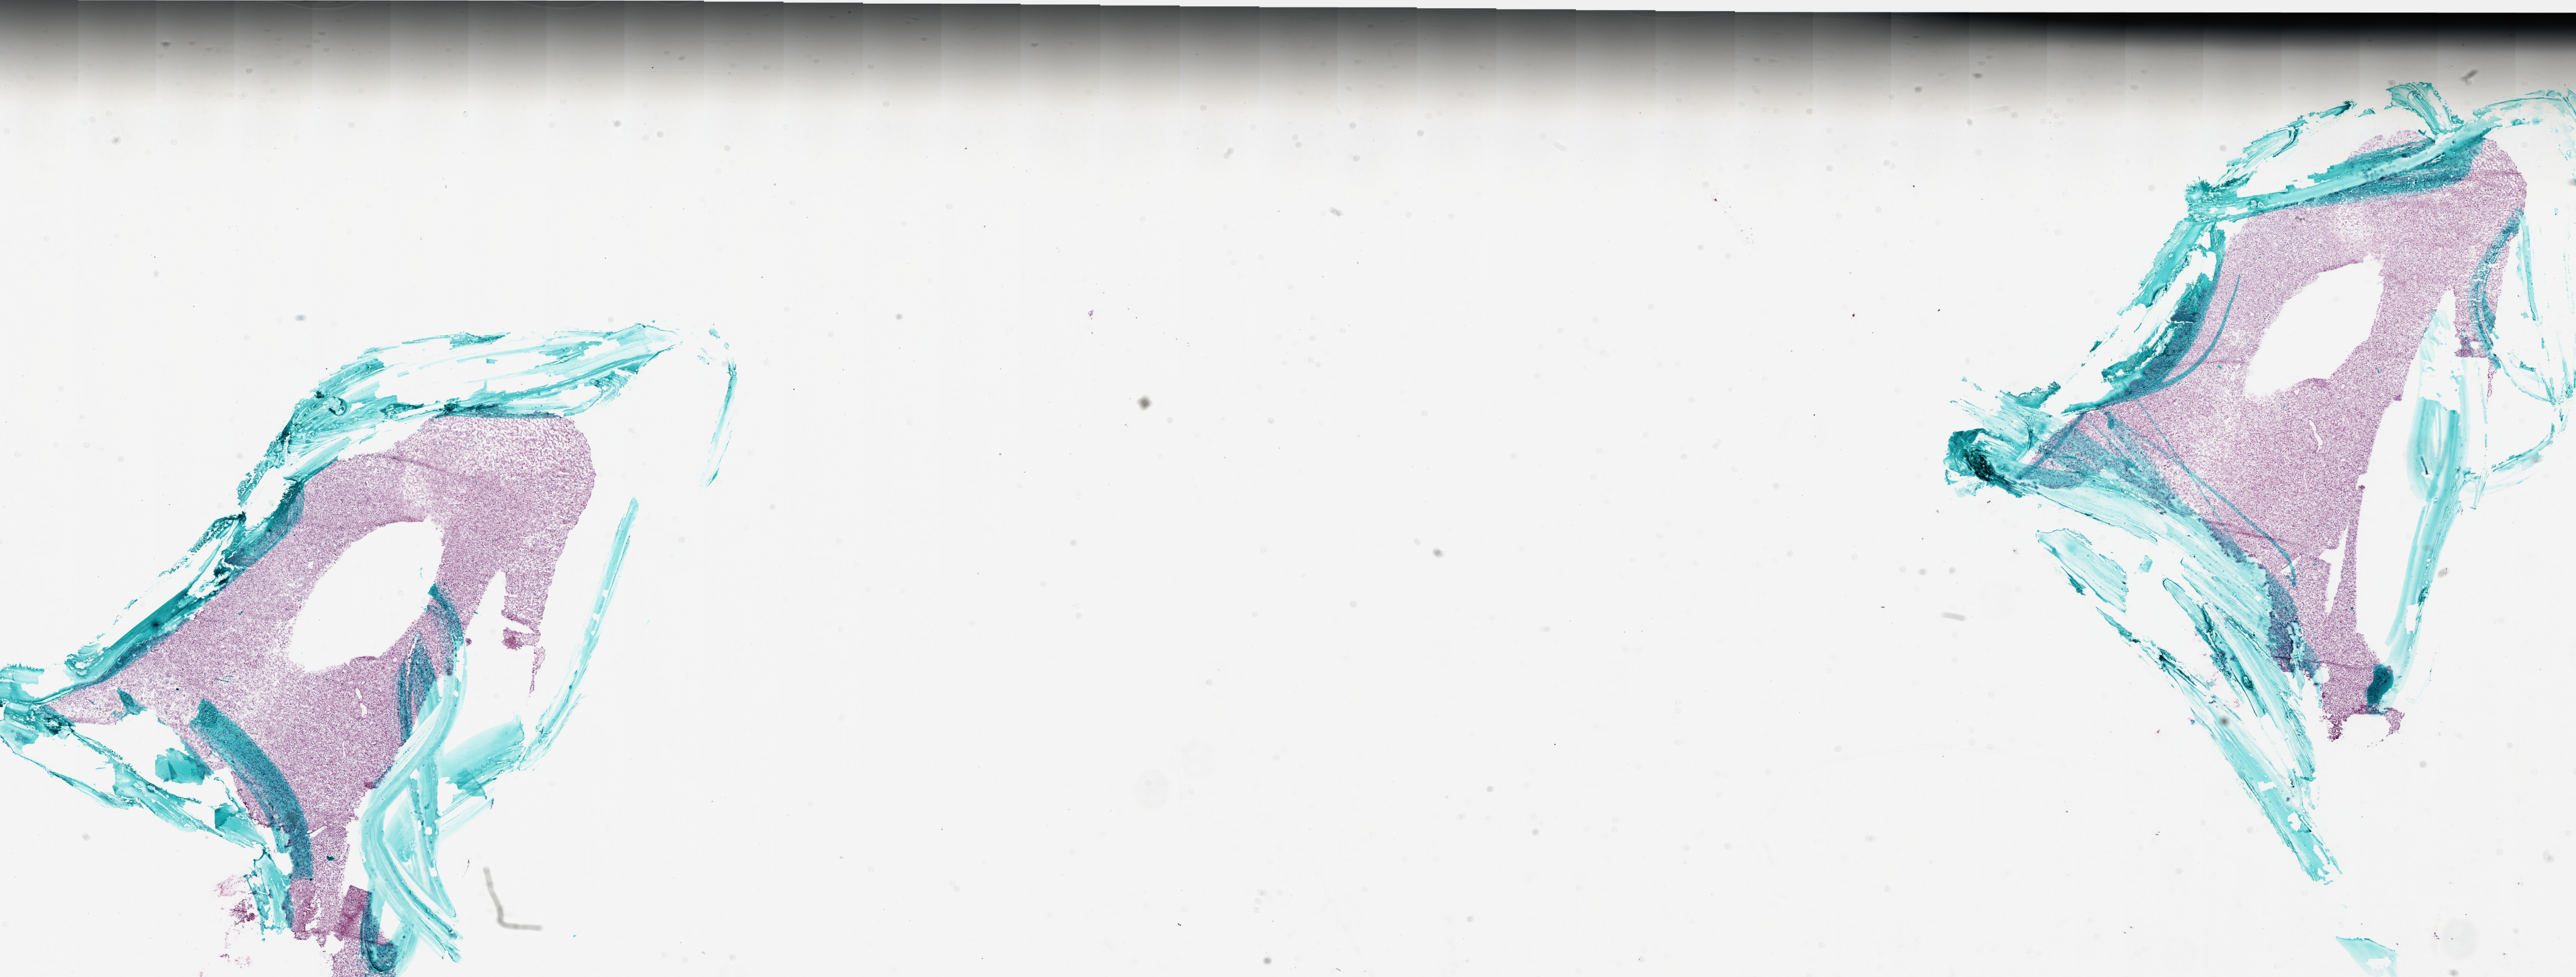
Digitized Hematoxylin and eosin (H&E) stained tissue section (whole slide), whole scanned area (about 33.0 x 12.5 mm, from a 20x scan) shown as a low-resolution overview. Frozen section from the bottom of the tissue portion. Sample: primary tumour, brain. Male, age 70 years at initial diagnosis.
Pathologic diagnosis: Glioblastoma.